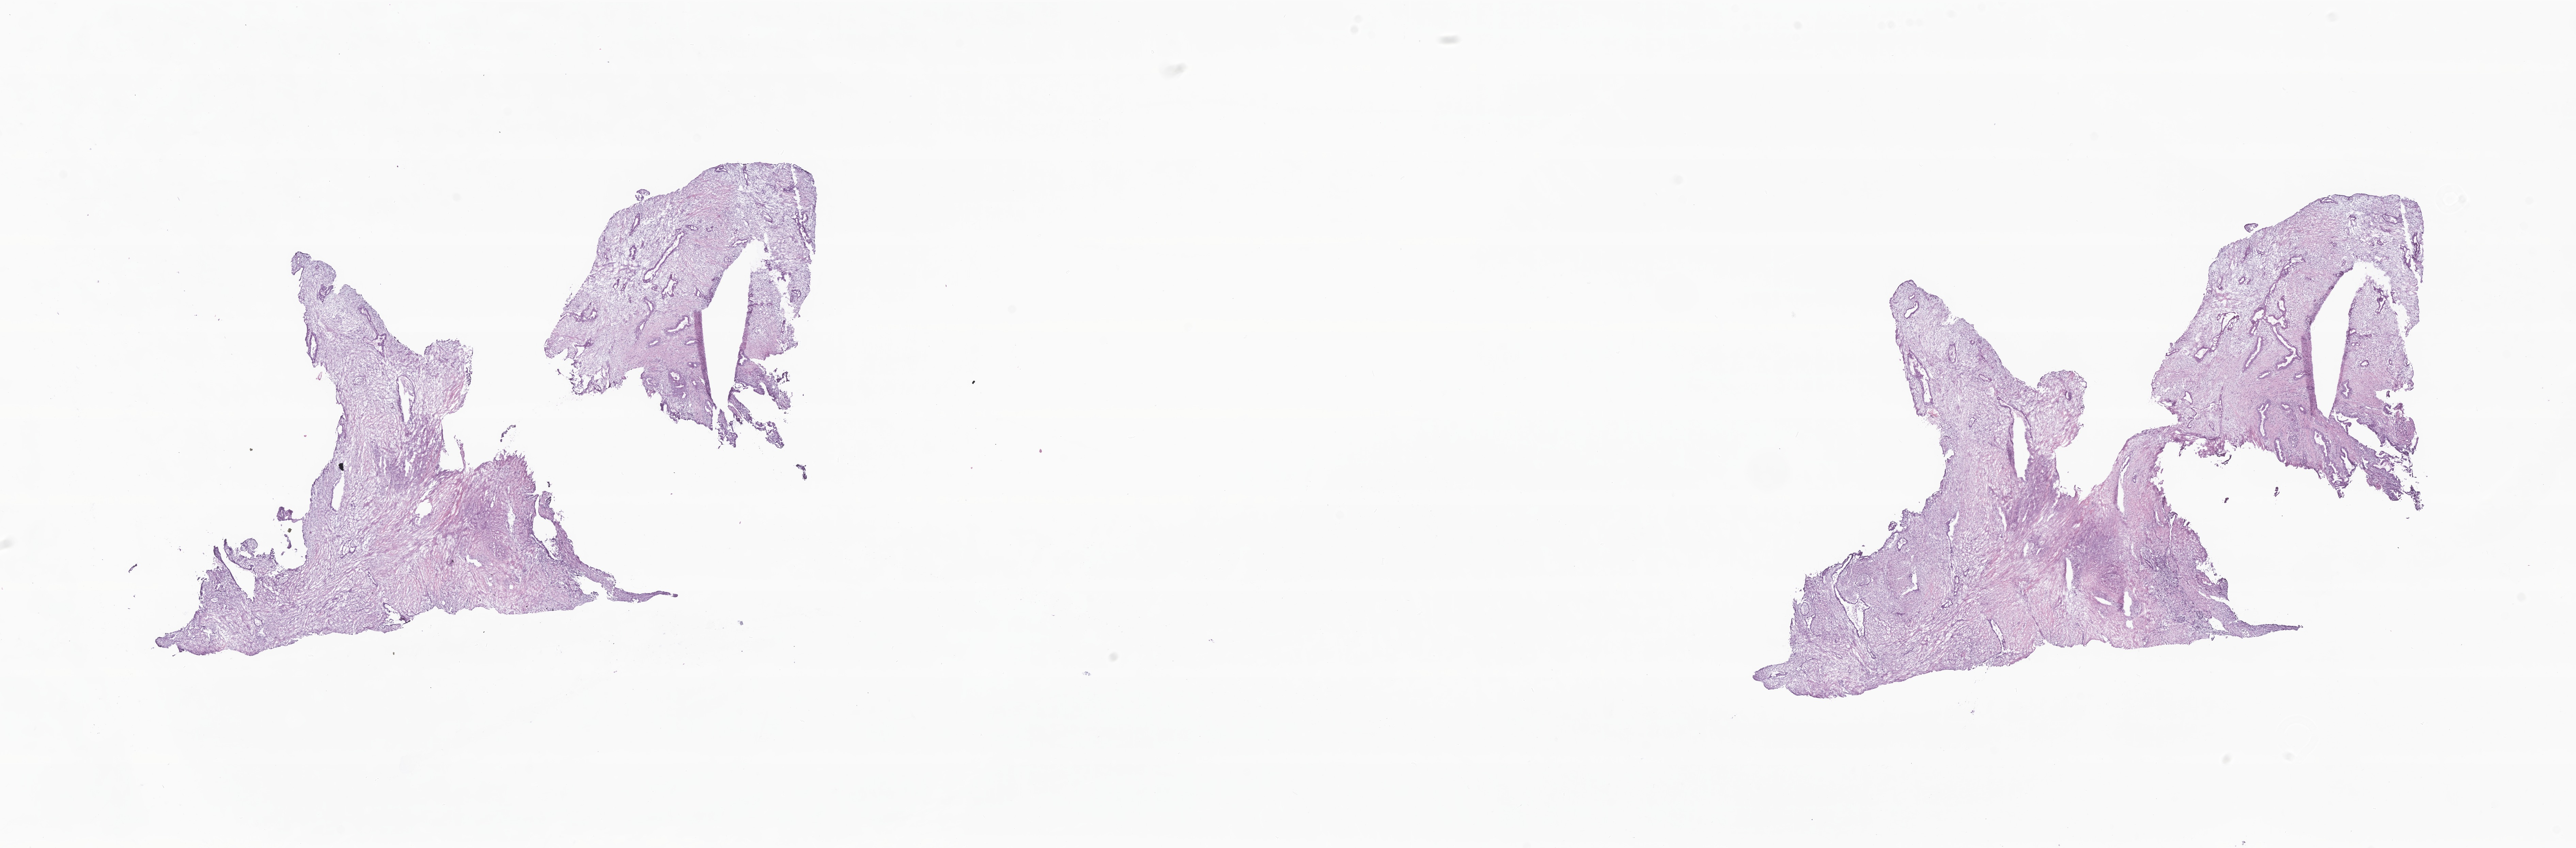
Digitized H&E-stained section, a low-resolution overview of the entire scanned area, about 31.9 x 10.5 mm. Frozen section (tissue freezing medium). Specimen: primary tumor. Anatomic site: tail of pancreas. Patient: male, age at initial diagnosis 68 years. Composition of this section per pathologist review: tumor cells 15%, tumor nuclei 20%, stromal cells 85%, necrosis 0%, normal cells 0%. Infiltration values recorded for this section: lymphocyte infiltration 0%, monocyte infiltration 0%, neutrophil infiltration 0%.
Histologic diagnosis: Infiltrating duct carcinoma, NOS.